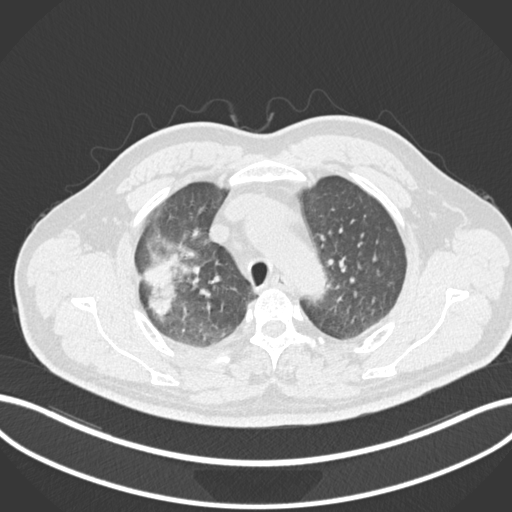
Chest CT, one axial slice; position 679 of 852 along the scan axis; reconstruction kernel B30f; 120 kVp; lung window (W 1500 / L -600 HU); 1 mm slice thickness; 512 × 512 image matrix. Male patient, age 55 years. From the clinical record (not read from this slice): clinical TNM (as recorded): T3 N2 M1.
Outlined on this slice (rectangle marked by the reading radiologist):
- lung tumour (recorded histology: adenocarcinoma): bounding box [x1, y1, x2, y2] px = [142, 259, 181, 322]